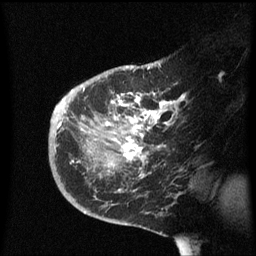
Breast MRI (dynamic contrast-enhanced), one sagittal slice; slice 38 of 60 in the series (ordered by position); dynamic contrast-enhanced series, image 2 of 3 at this slice position (ordered by acquisition); 1.5 T; TE 4.2 ms, TR 8.4 ms; 2.3 mm slice thickness; 256 × 256 image matrix, field of view 200 × 200 mm. Female patient, age 38 years. Case-level facts recorded for this patient, not image findings: setting: breast cancer imaged before/during neoadjuvant chemotherapy; receptor status: HER2-positive.
Annotated regions visible in this slice (semi-automatic segmentation, software-assisted and operator-edited):
- analysis volume of interest (the breast-tissue region the enhancement analysis was run in; not a lesion): bounding box <49,78,191,213> (left, top, right, bottom; pixels)
- tumour enhancement mask (voxels above the 70 % enhancement threshold inside the analysis volume of interest): <59,92,178,163>